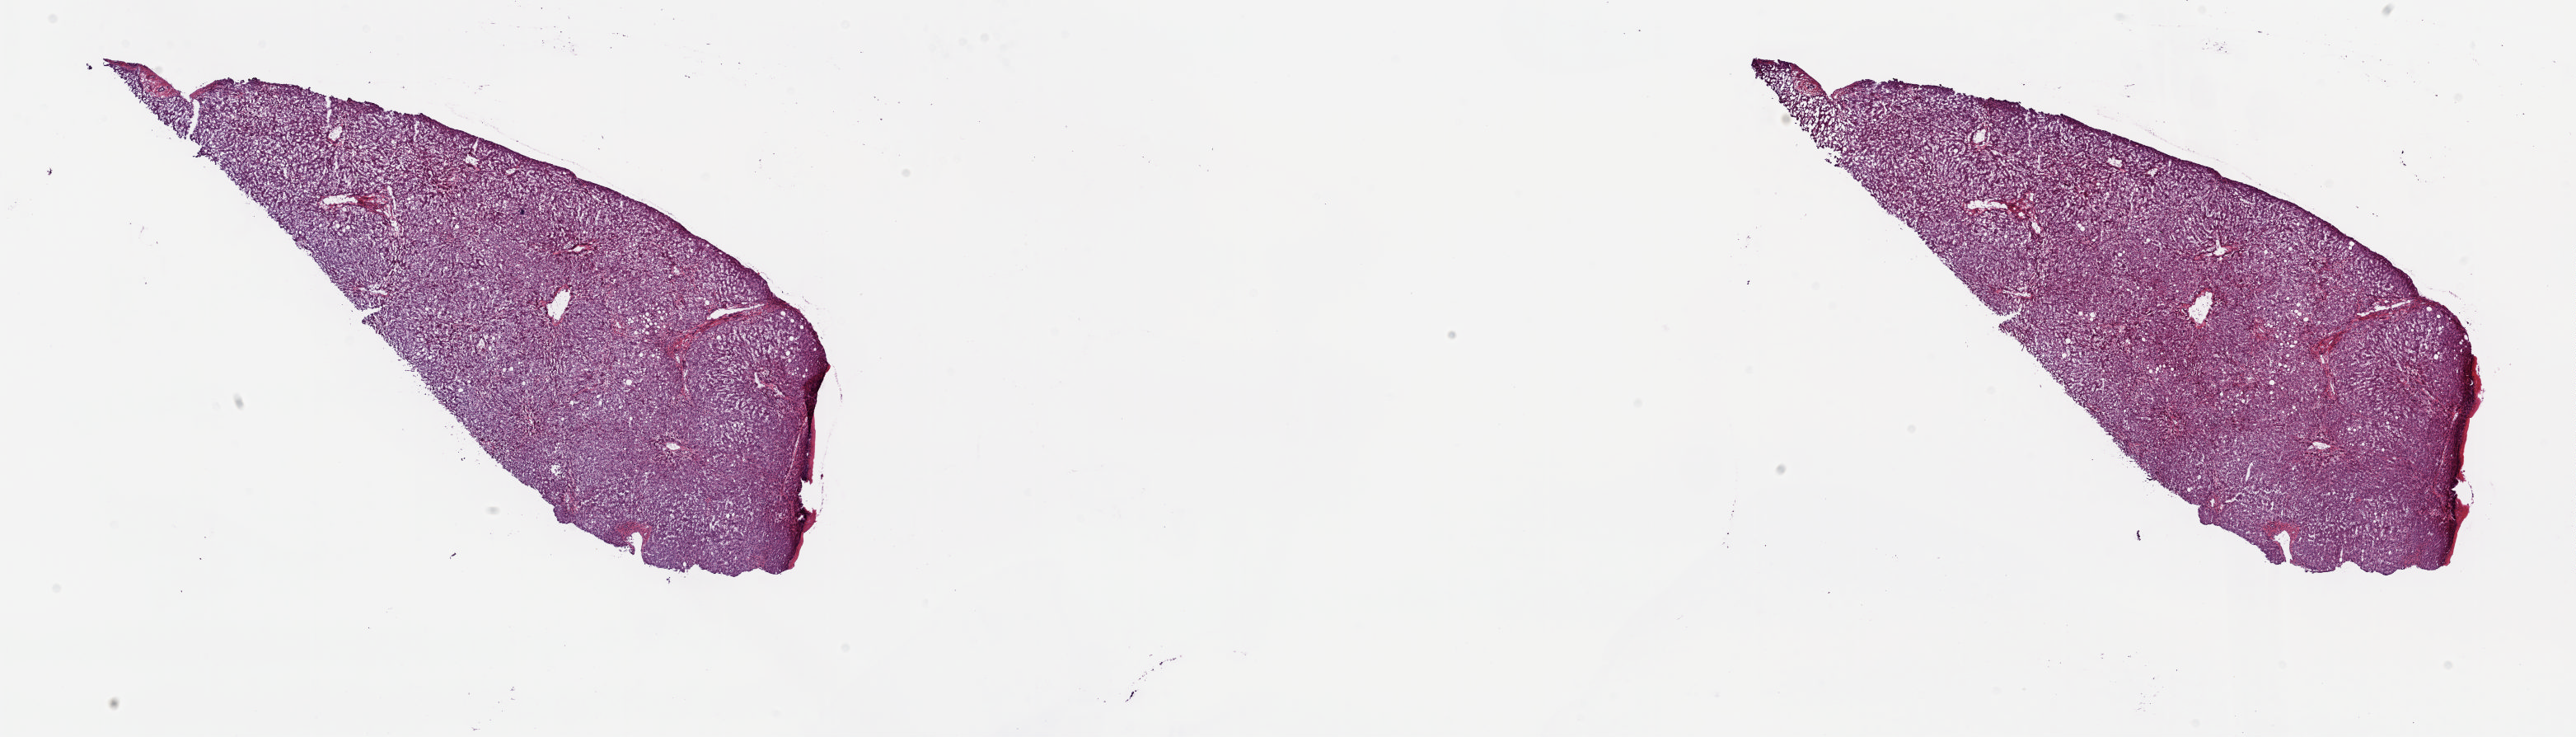
Whole-slide histology image, H&E-stained — a low-resolution overview of the entire scanned area, about 24.8 x 7.1 mm; frozen section from the top of the tissue portion; bile duct, solid tissue normal (non-tumour tissue) sample. Male patient; age at initial diagnosis 68 years. Composition of this section per pathologist review: tumour cells 0%, tumour nuclei 0%, normal cells 80%, stromal cells 20%, necrosis 0%. Inflammatory infiltration, as recorded: lymphocyte infiltration 4%, monocyte infiltration 1%, neutrophil infiltration 2%.
• this section: solid tissue normal (non-tumour) sample from the same patient
• patient diagnosis: Cholangiocarcinoma (intrahepatic bile duct)